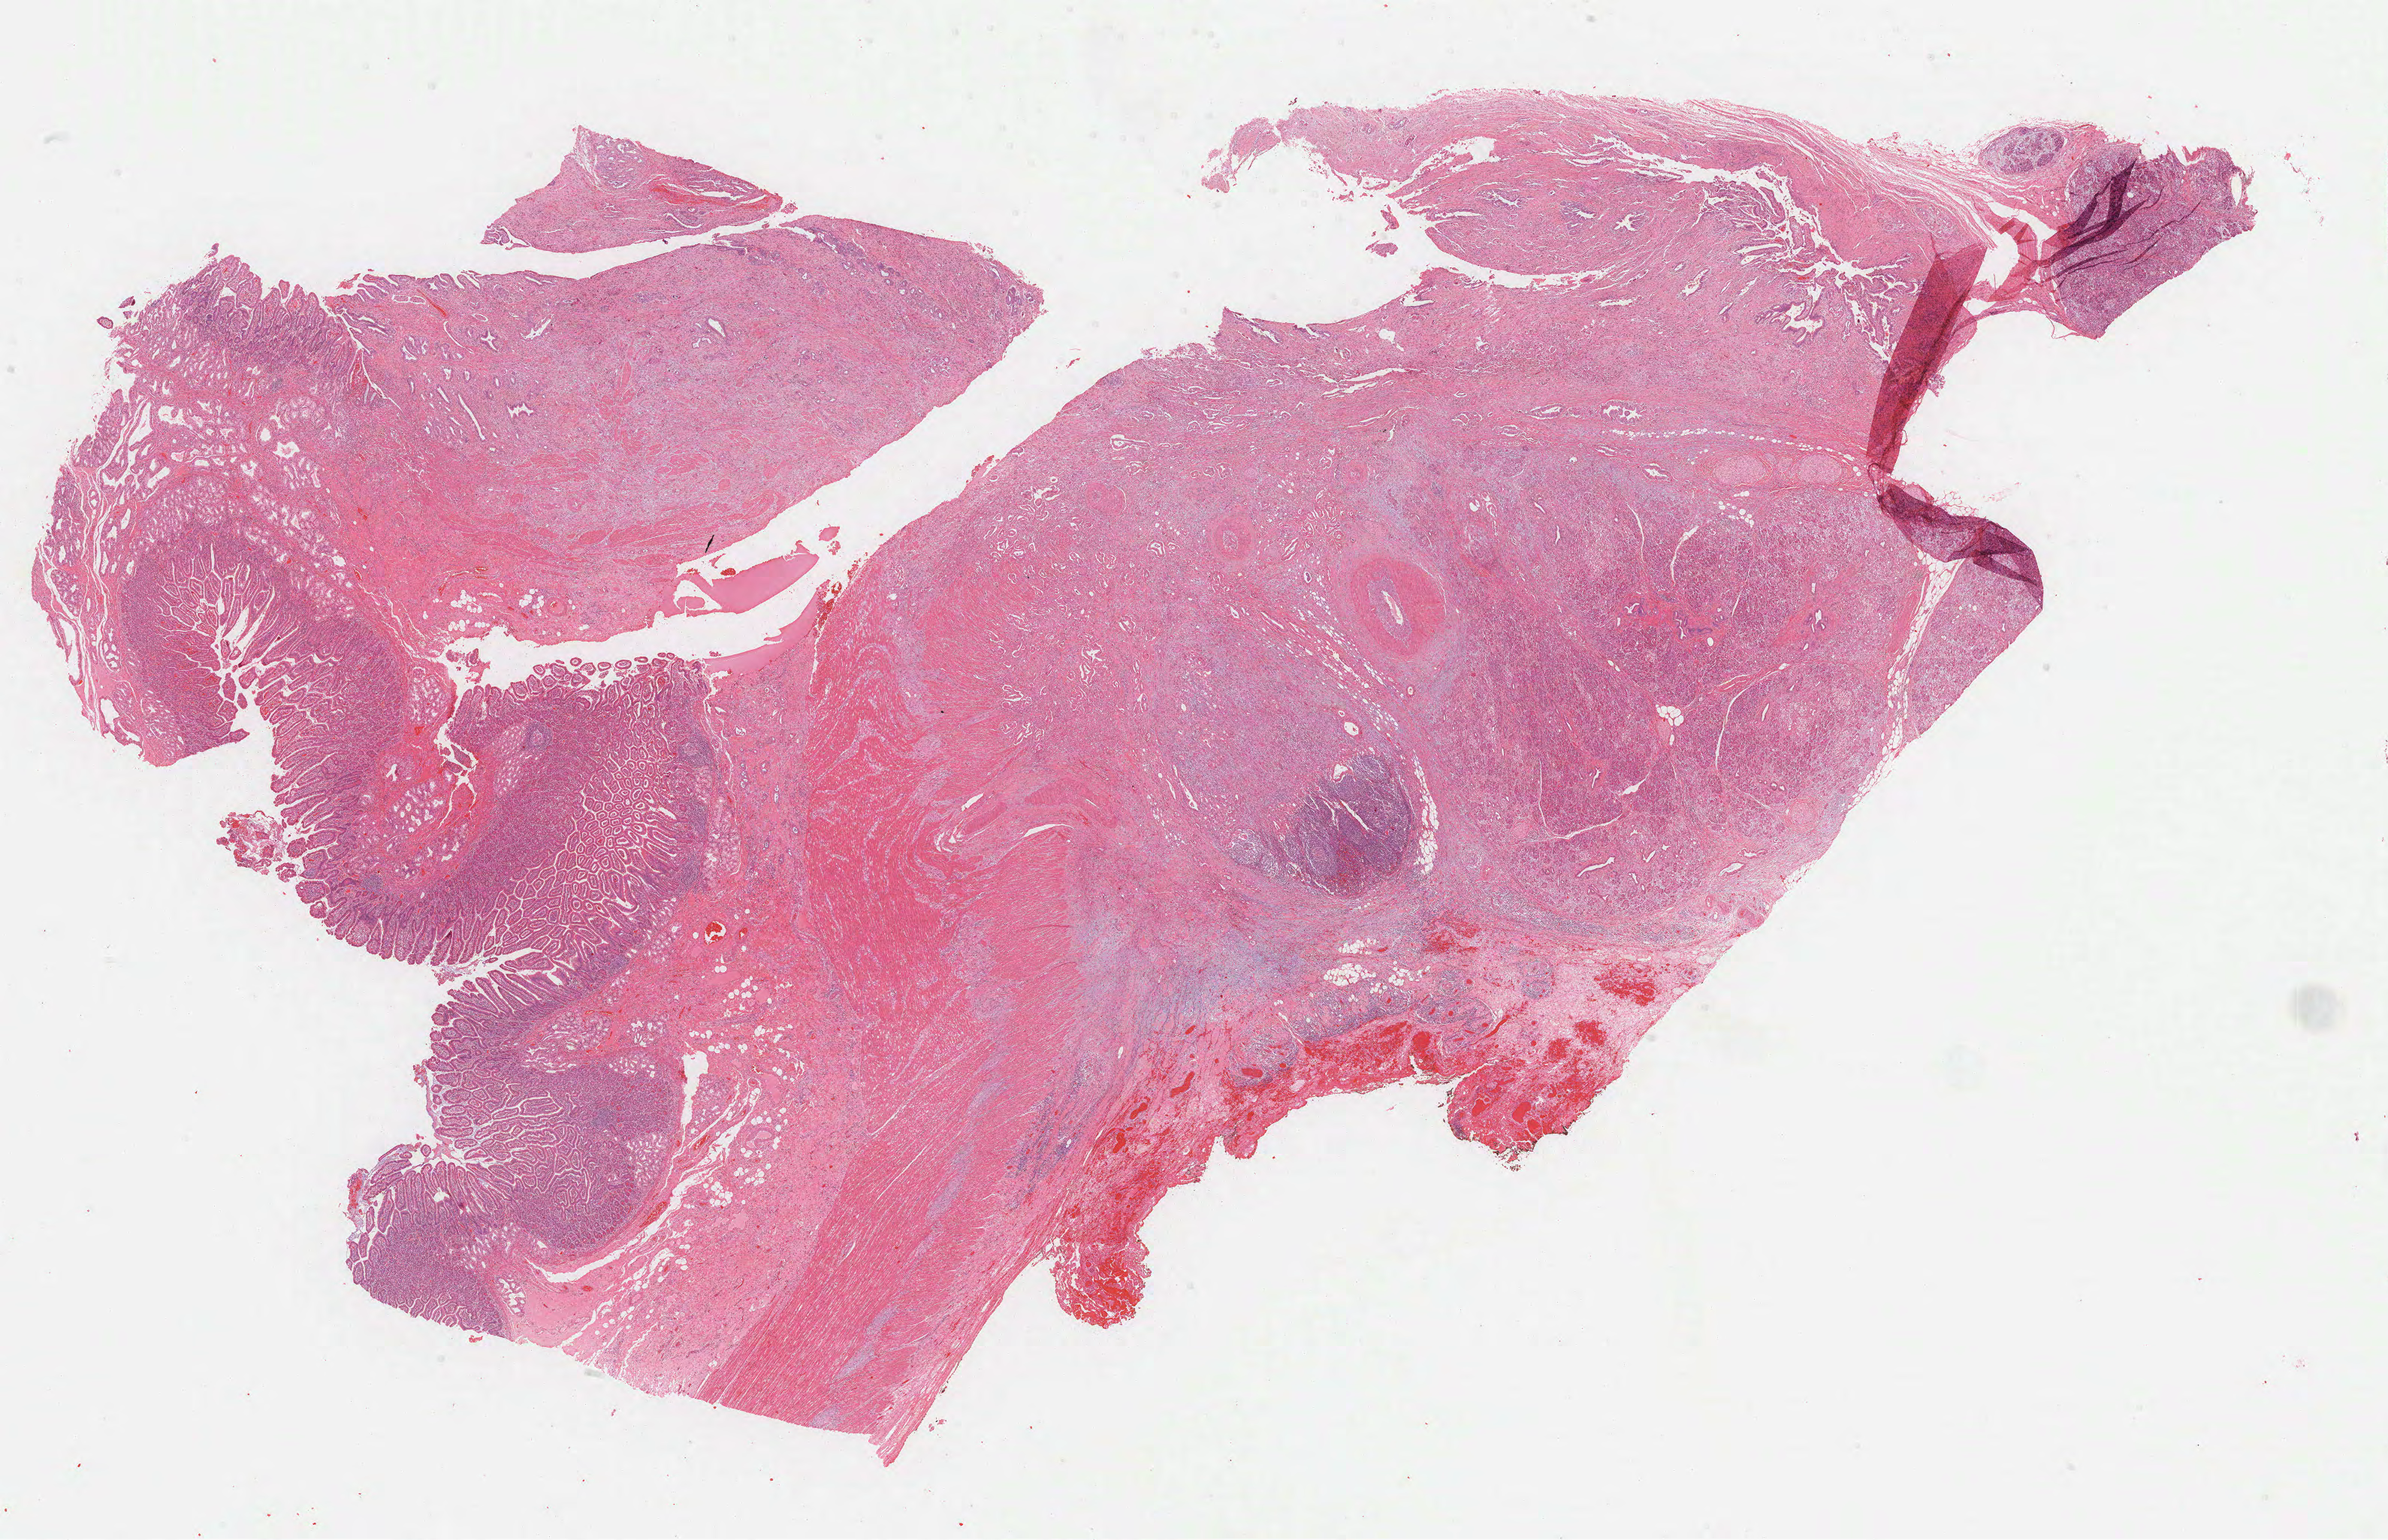
Whole-slide histology image, H&E, whole scanned area (about 25.7 x 16.6 mm, slide scanned at 40x) shown as a low-resolution overview; formalin-fixed paraffin-embedded (FFPE) diagnostic section; pancreas, primary tumour sample. Male patient; age at initial diagnosis 45 years. Histologic grade: G2 (moderately differentiated).
- AJCC pathologic stage: IIB
- histologic diagnosis: Infiltrating duct carcinoma, NOS (head of pancreas)